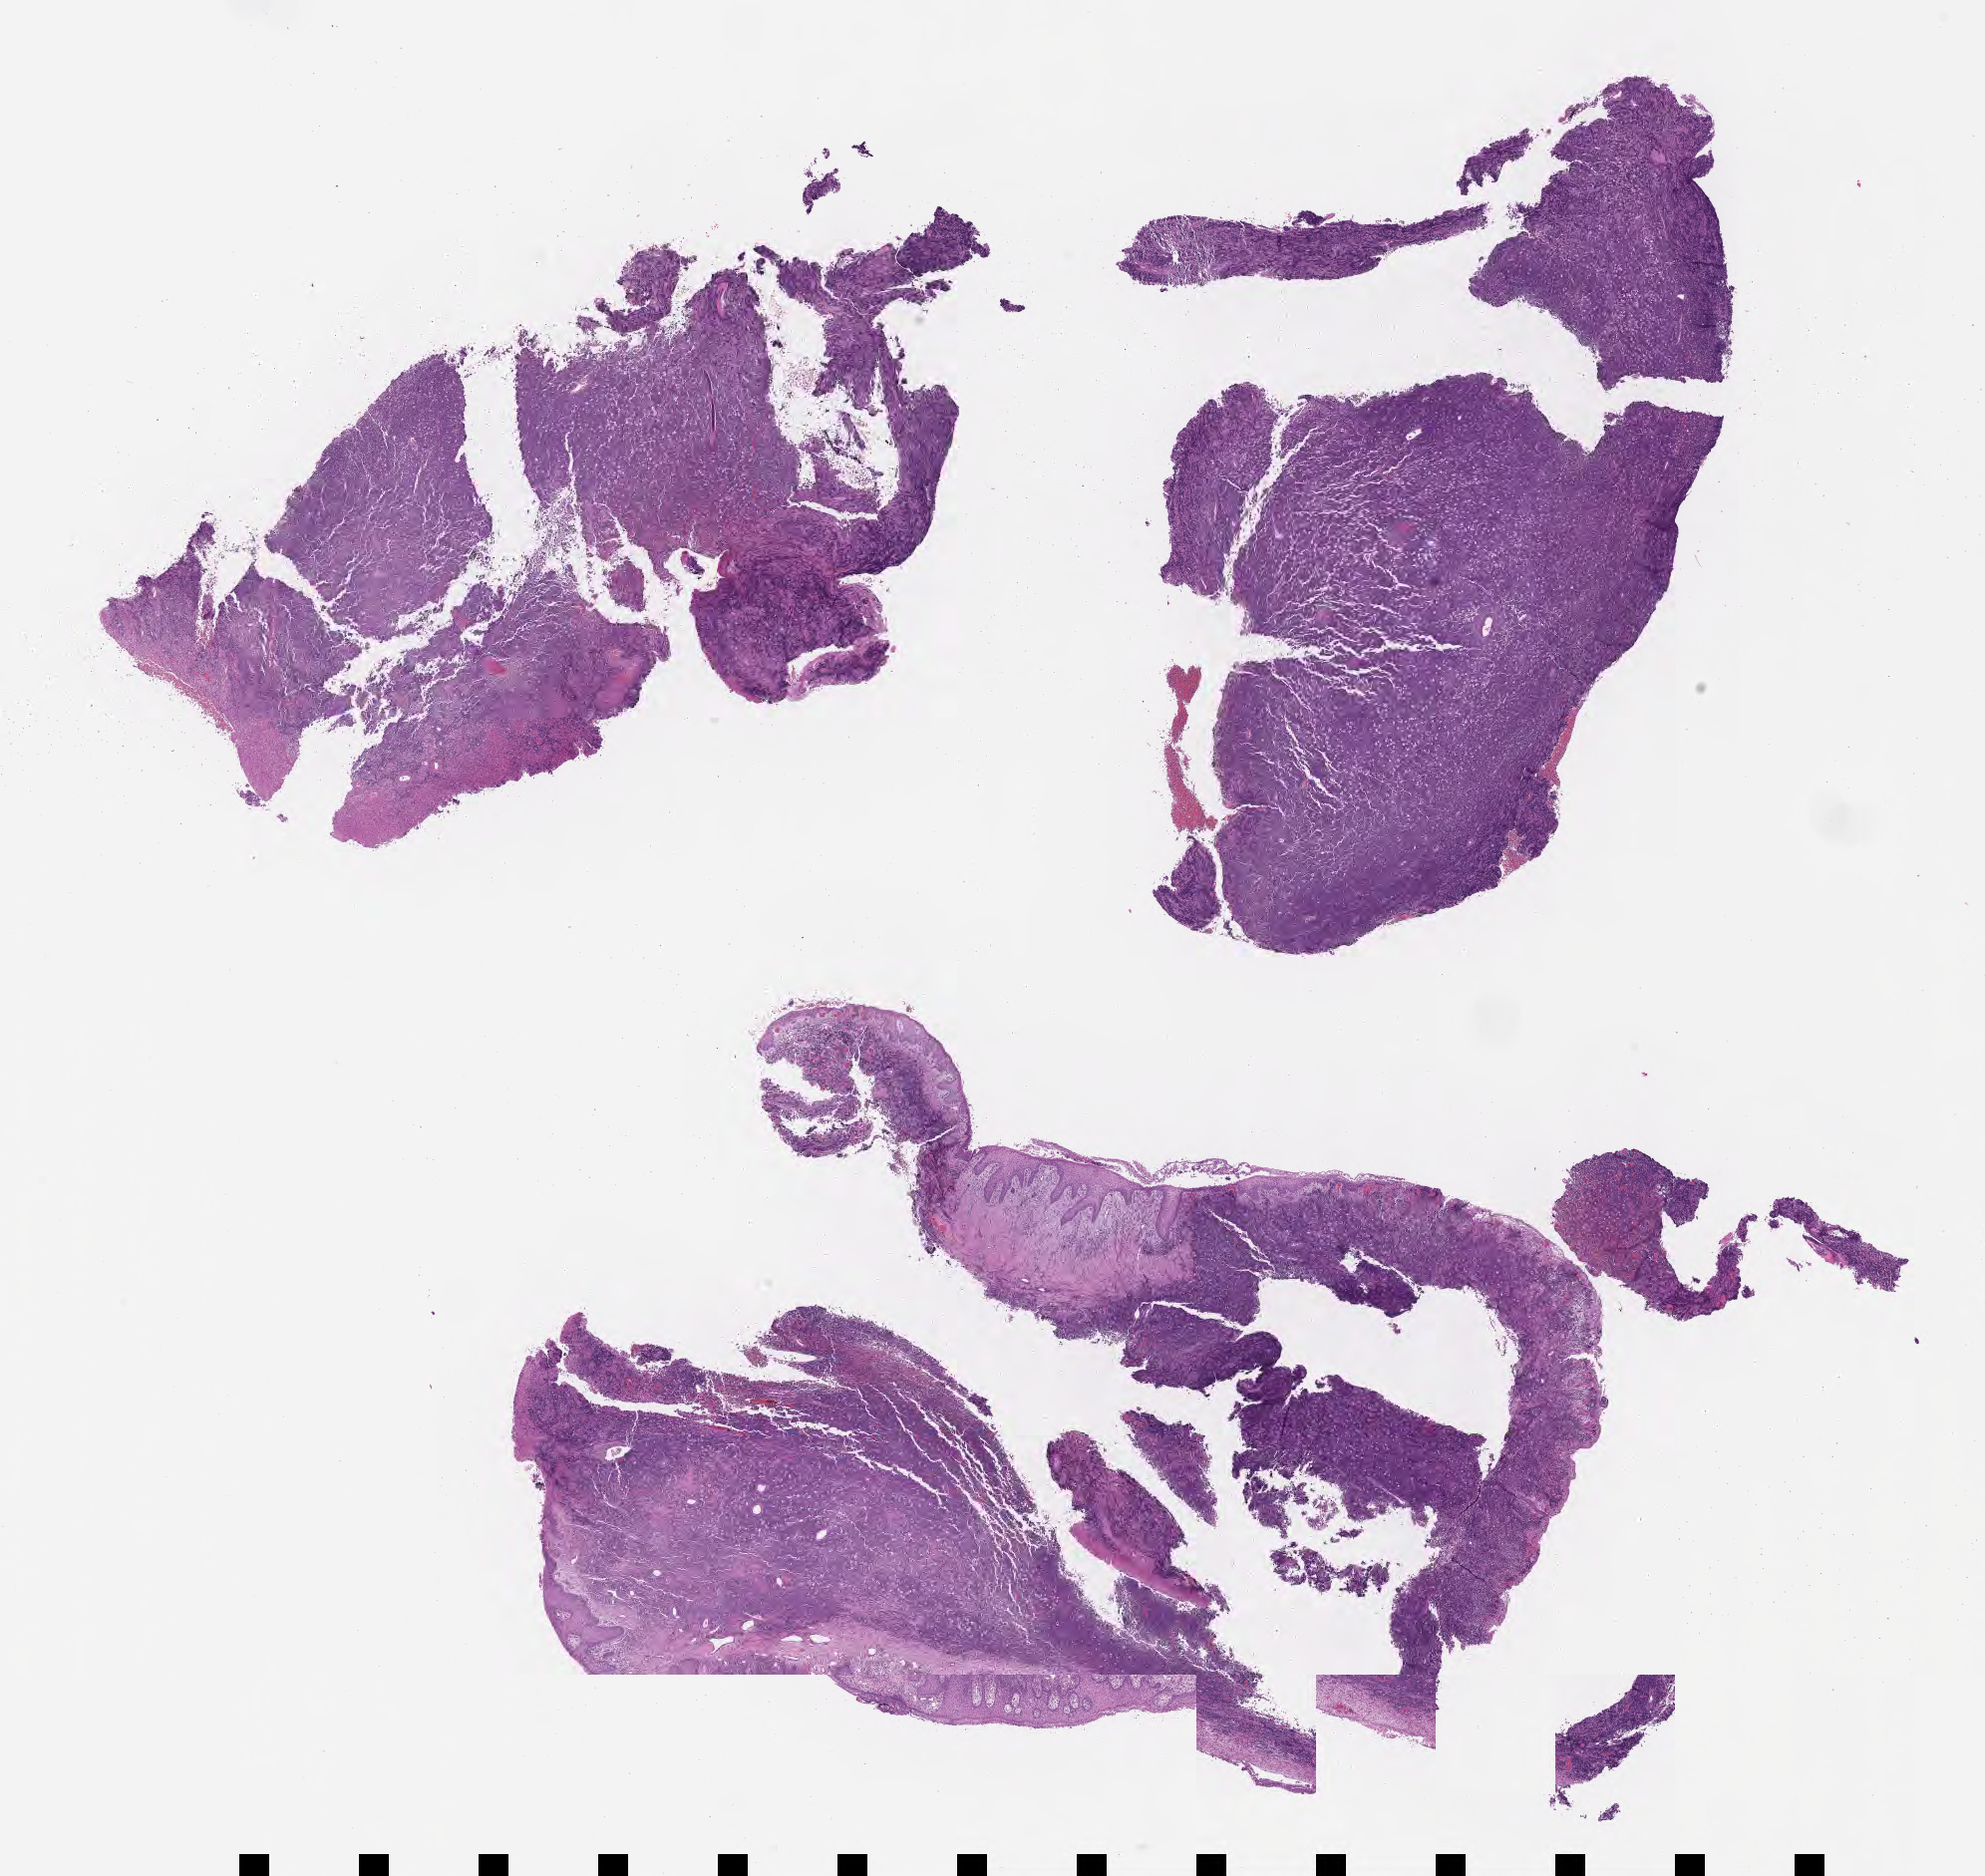
H&E whole-slide image — shown as a low-resolution overview of the whole scanned area (about 16.1 x 15.2 mm); formalin-fixed paraffin-embedded section; primary tumor. Male patient, 22 years old.
Histologic diagnosis: Burkitt lymphoma, NOS.